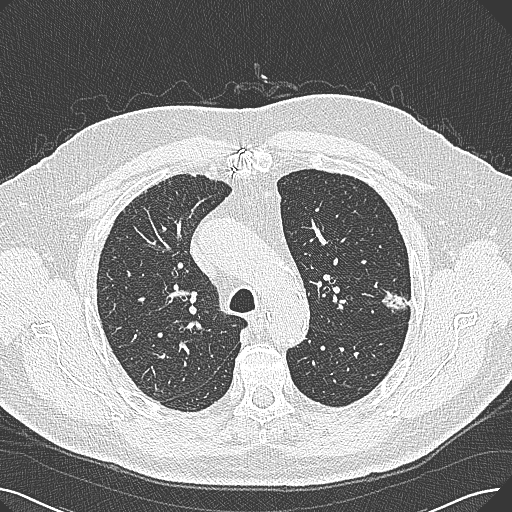
Low-dose screening chest CT, axial slice; first (baseline) screen; lung window (W 1500 / L -600 HU); 1 mm slice thickness; 512 × 512 image matrix, field of view 370 × 370 mm. Male, age 74 years at enrolment. Former smoker at enrolment.
• Expert-annotated lung lesion, bounding box (x1, y1, x2, y2) in pixels: (372, 273, 424, 320).
• Screening reader's record for this exam (one nodule recorded; not confirmed to be the boxed lesion): non-calcified nodule or mass ≥4 mm, left upper lobe, 15 × 10 mm, poorly defined margins, soft tissue attenuation.
• Official screen result: positive, change unspecified: nodule(s) >= 4 mm or enlarging nodule(s), mass(es), or other non-specific abnormalities suspicious for lung cancer.
• Lung cancer was diagnosed 124 days after this screen: adenocarcinoma, NOS, left upper lobe, well differentiated (G1), stage IA (AJCC 6th edition), 26 mm at pathology.